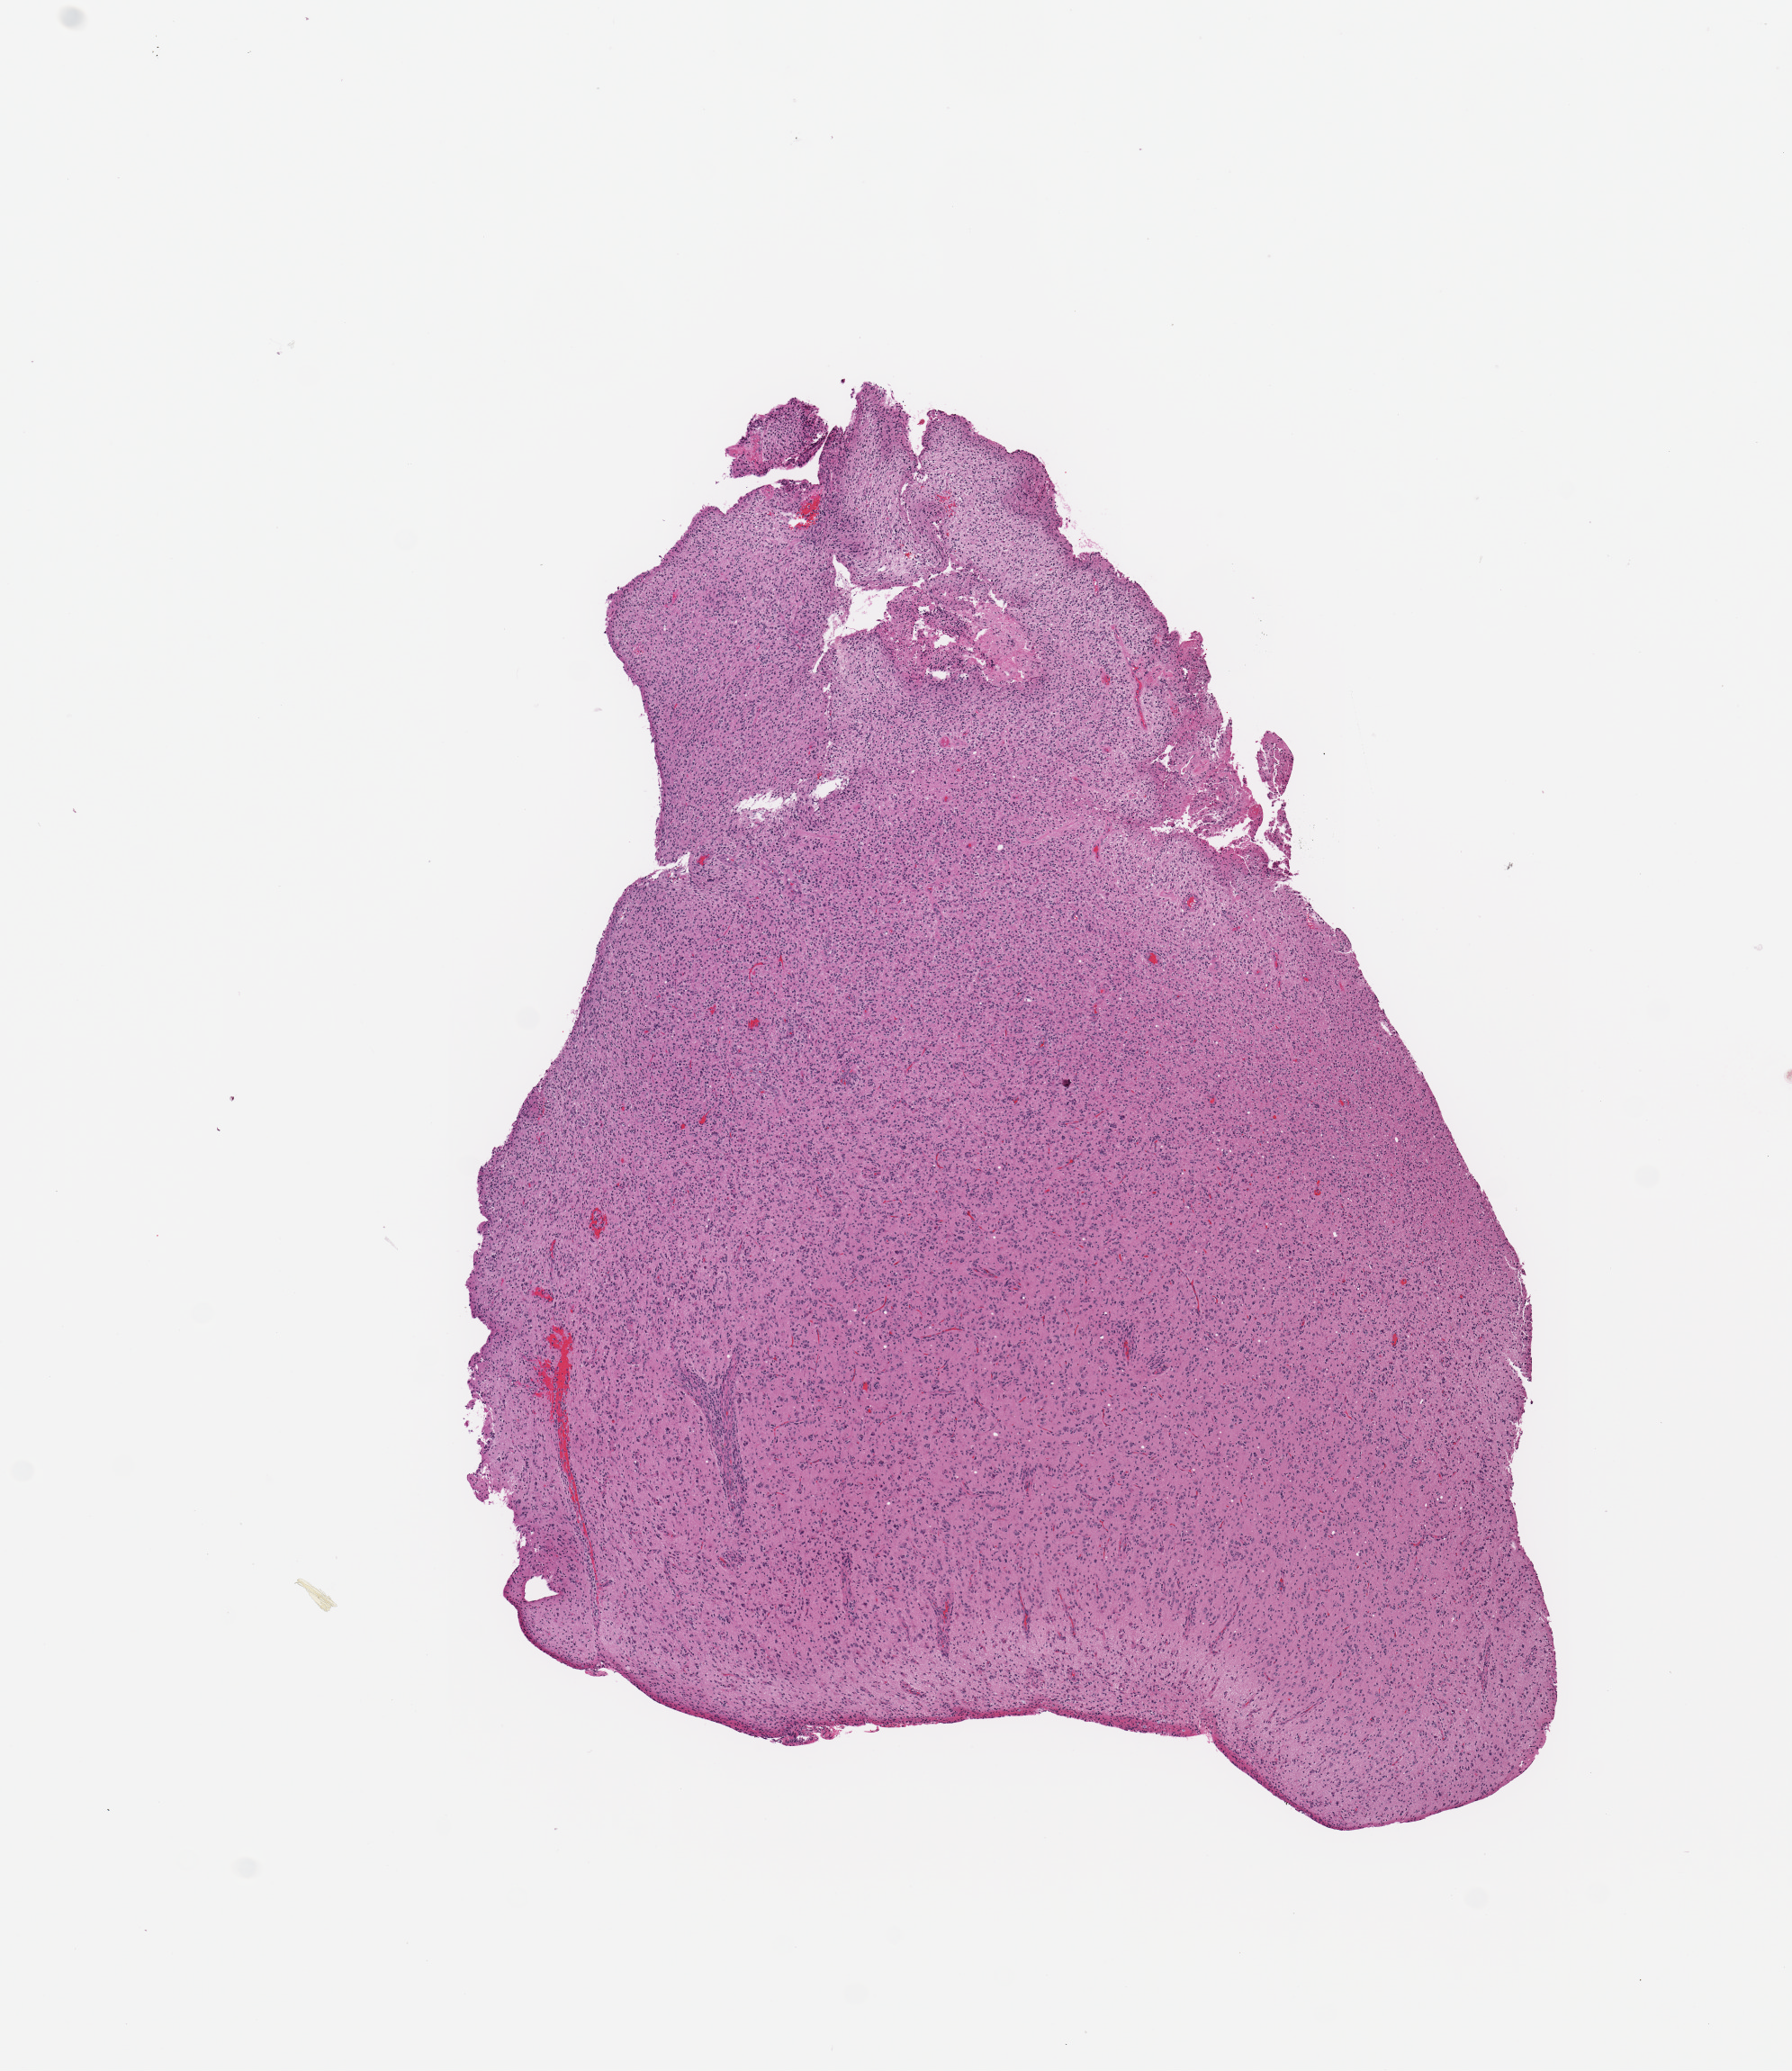
Digitized H&E-stained tissue section (whole slide), shown as a low-resolution overview of the whole scanned area (about 7.9 x 9.1 mm); tumour tissue sample, sampled site: brain. Male, 57 y/o.
Histologic diagnosis: Glioblastoma.